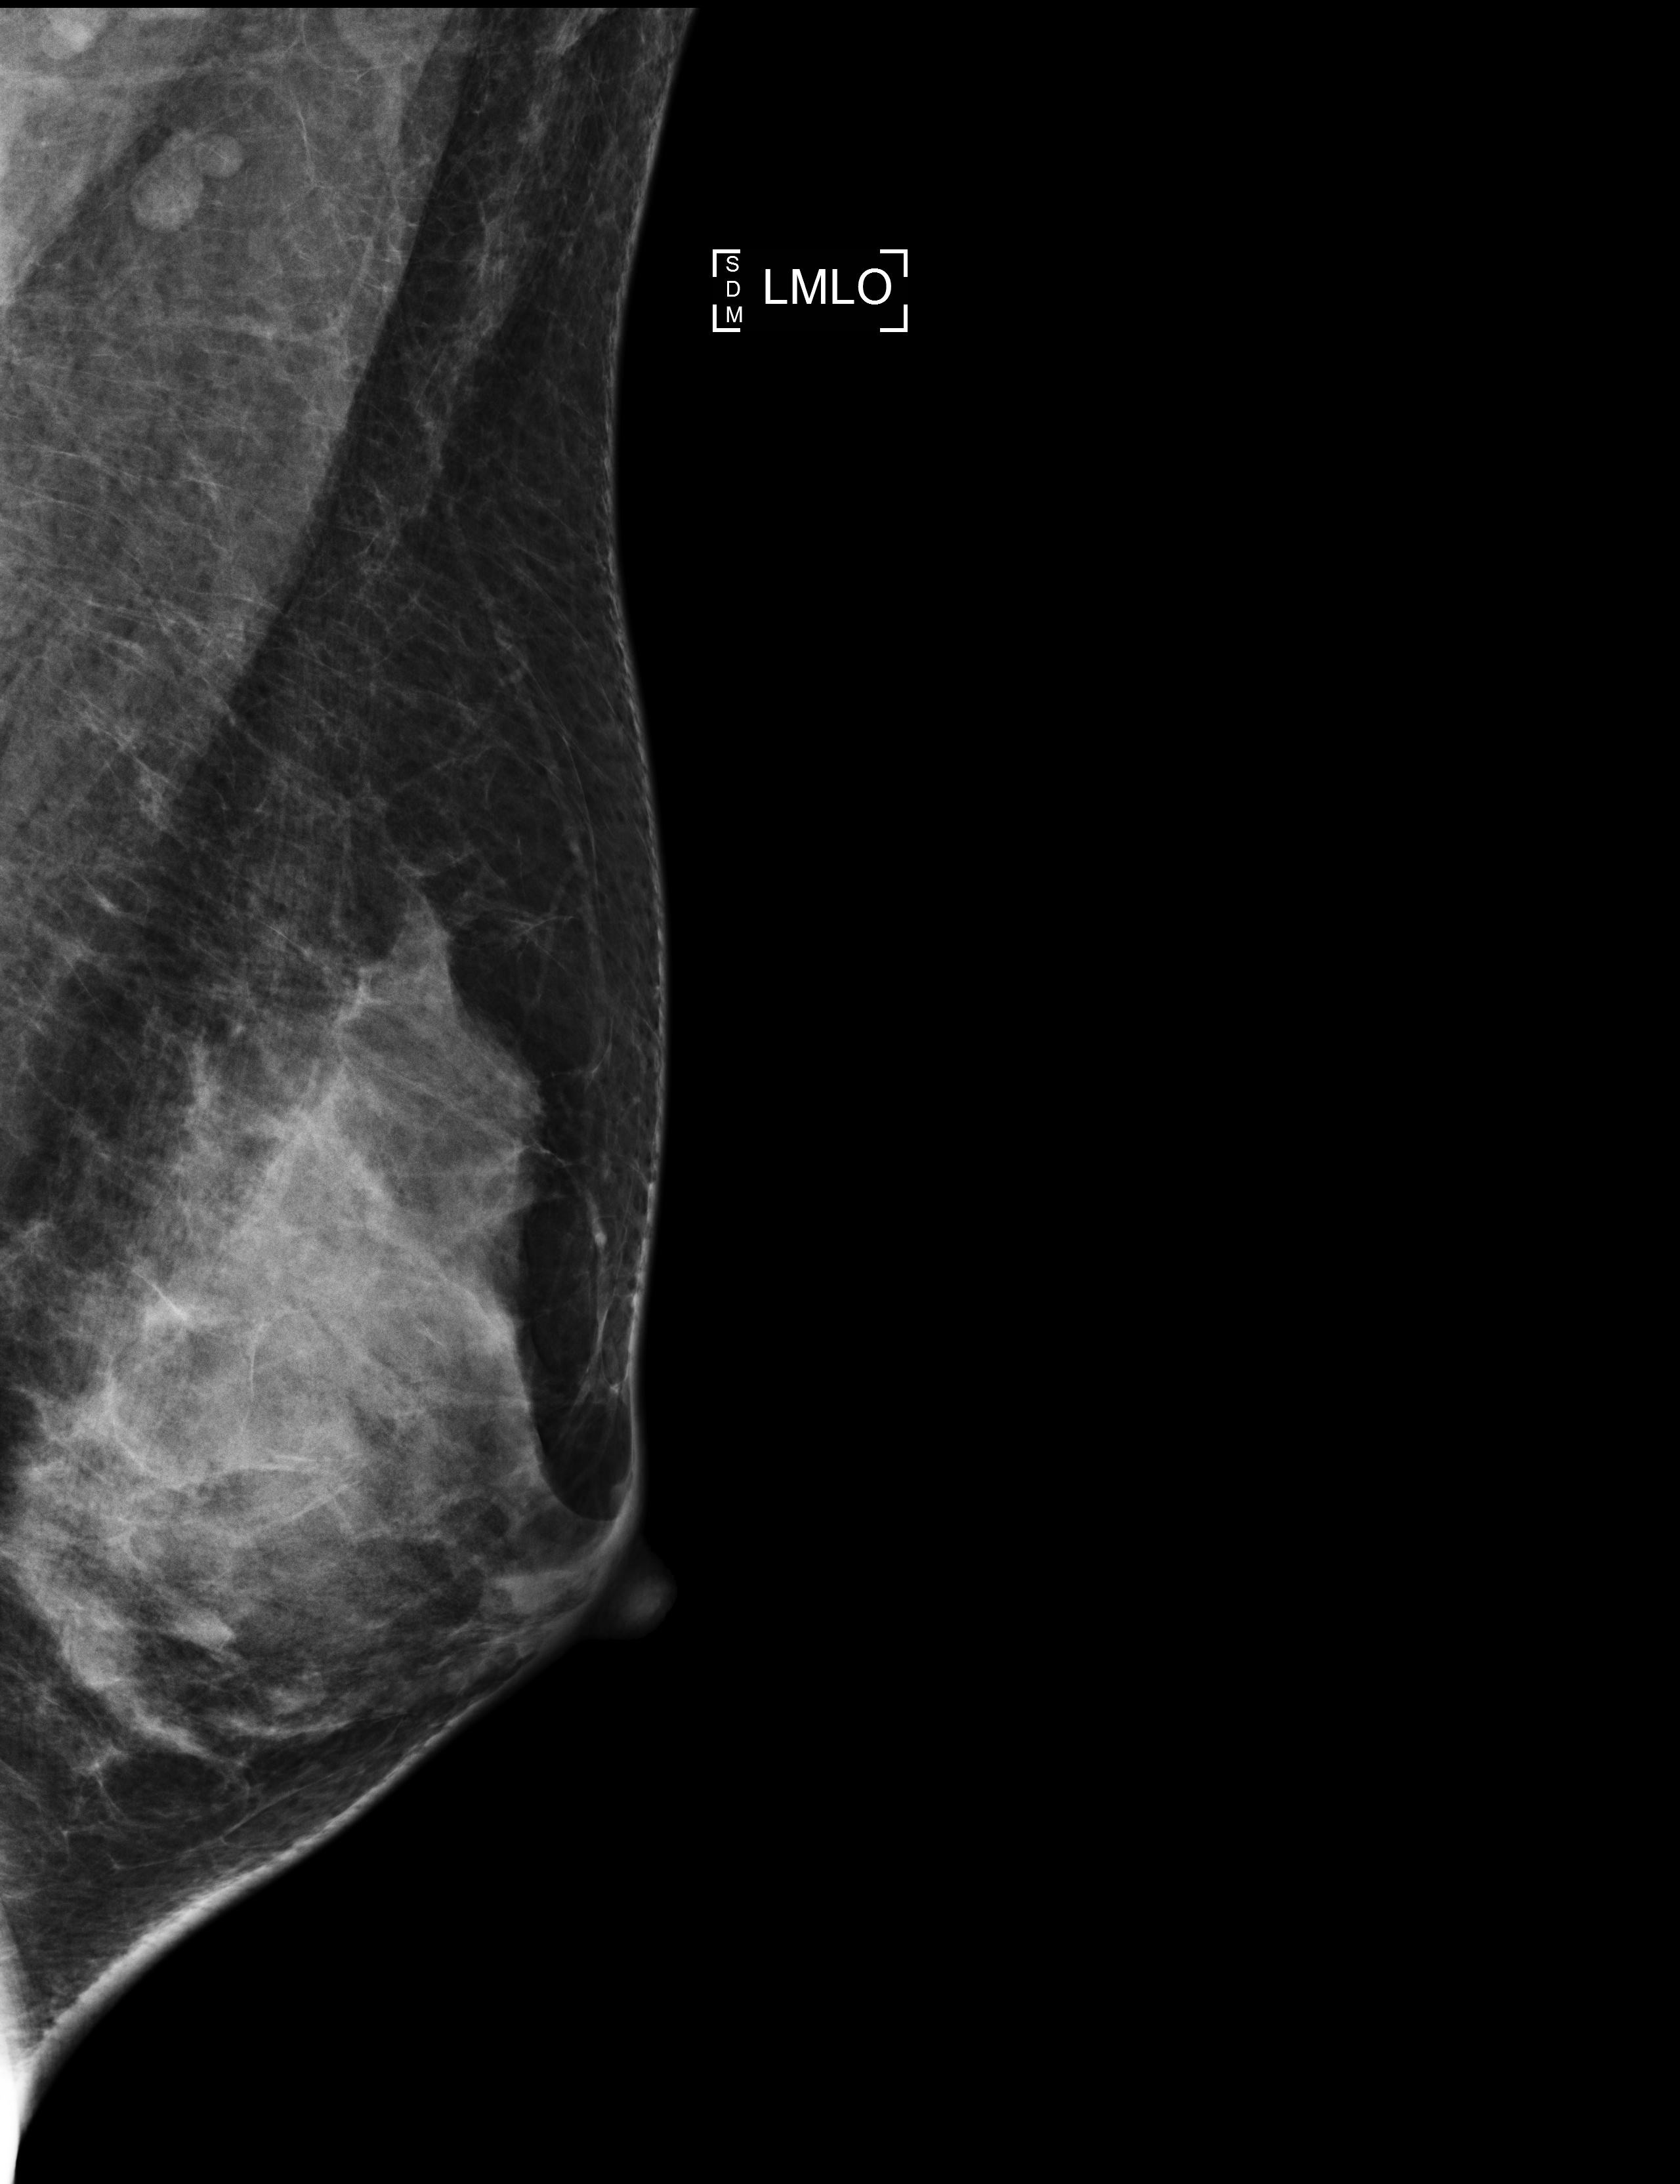
Digital mammogram (FFDM); left breast; mediolateral oblique (MLO) view; annual screening mammography examination; compressed breast thickness 59 mm; system: Selenia Dimensions. Patient aged 43 years (female).
BI-RADS breast density category at the screening exam (both breasts, scale 1–4): 3. Final BI-RADS category for the screening round (tomosynthesis exam, both breasts): category 1. Recall: recalled for additional imaging after this screen.